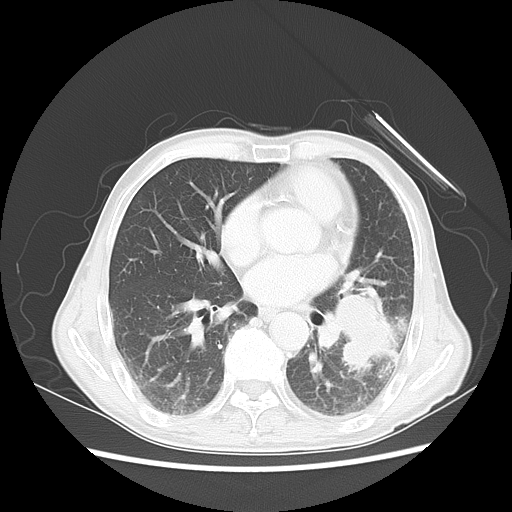
Chest CT, one axial slice; 120 kVp; lung window (W 1500 / L -600 HU); 5 mm slice thickness; 512 × 512 image matrix, field of view 360 × 360 mm. Male patient, age 64 years. From the clinical record (not read from this slice): clinical TNM (as recorded): T4 N0 M0.
Annotated regions visible in this slice (bounding box drawn by a radiologist):
- lung tumour (recorded histology: squamous cell carcinoma): box from (x=310, y=279) to (x=392, y=377) px